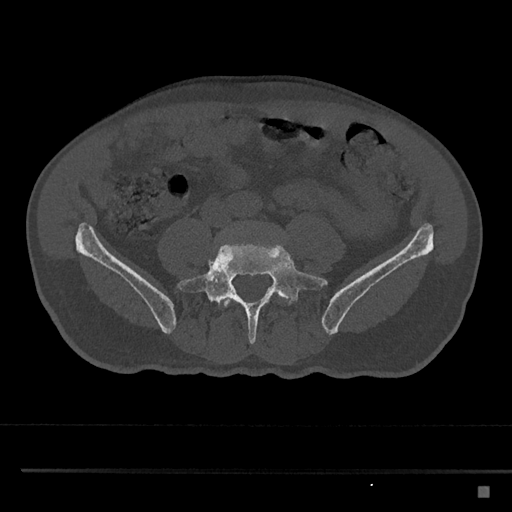
CT including the spine, one axial slice; slice 593 of 797 in the series (ordered by position); 120 kVp; bone window (W 1800 / L 400 HU); 0.5 mm slice thickness; 512 × 512 image matrix, field of view 391 × 391 mm. Male patient, age 59 years. Case-level facts recorded for this patient, not image findings: primary cancer: prostate.
Annotated regions visible in this slice (semi-automatically segmented with operator editing):
- L4 vertebra: bounding box <220,235,231,307> (left, top, right, bottom; pixels)
- L5 vertebra: <177,238,328,344>